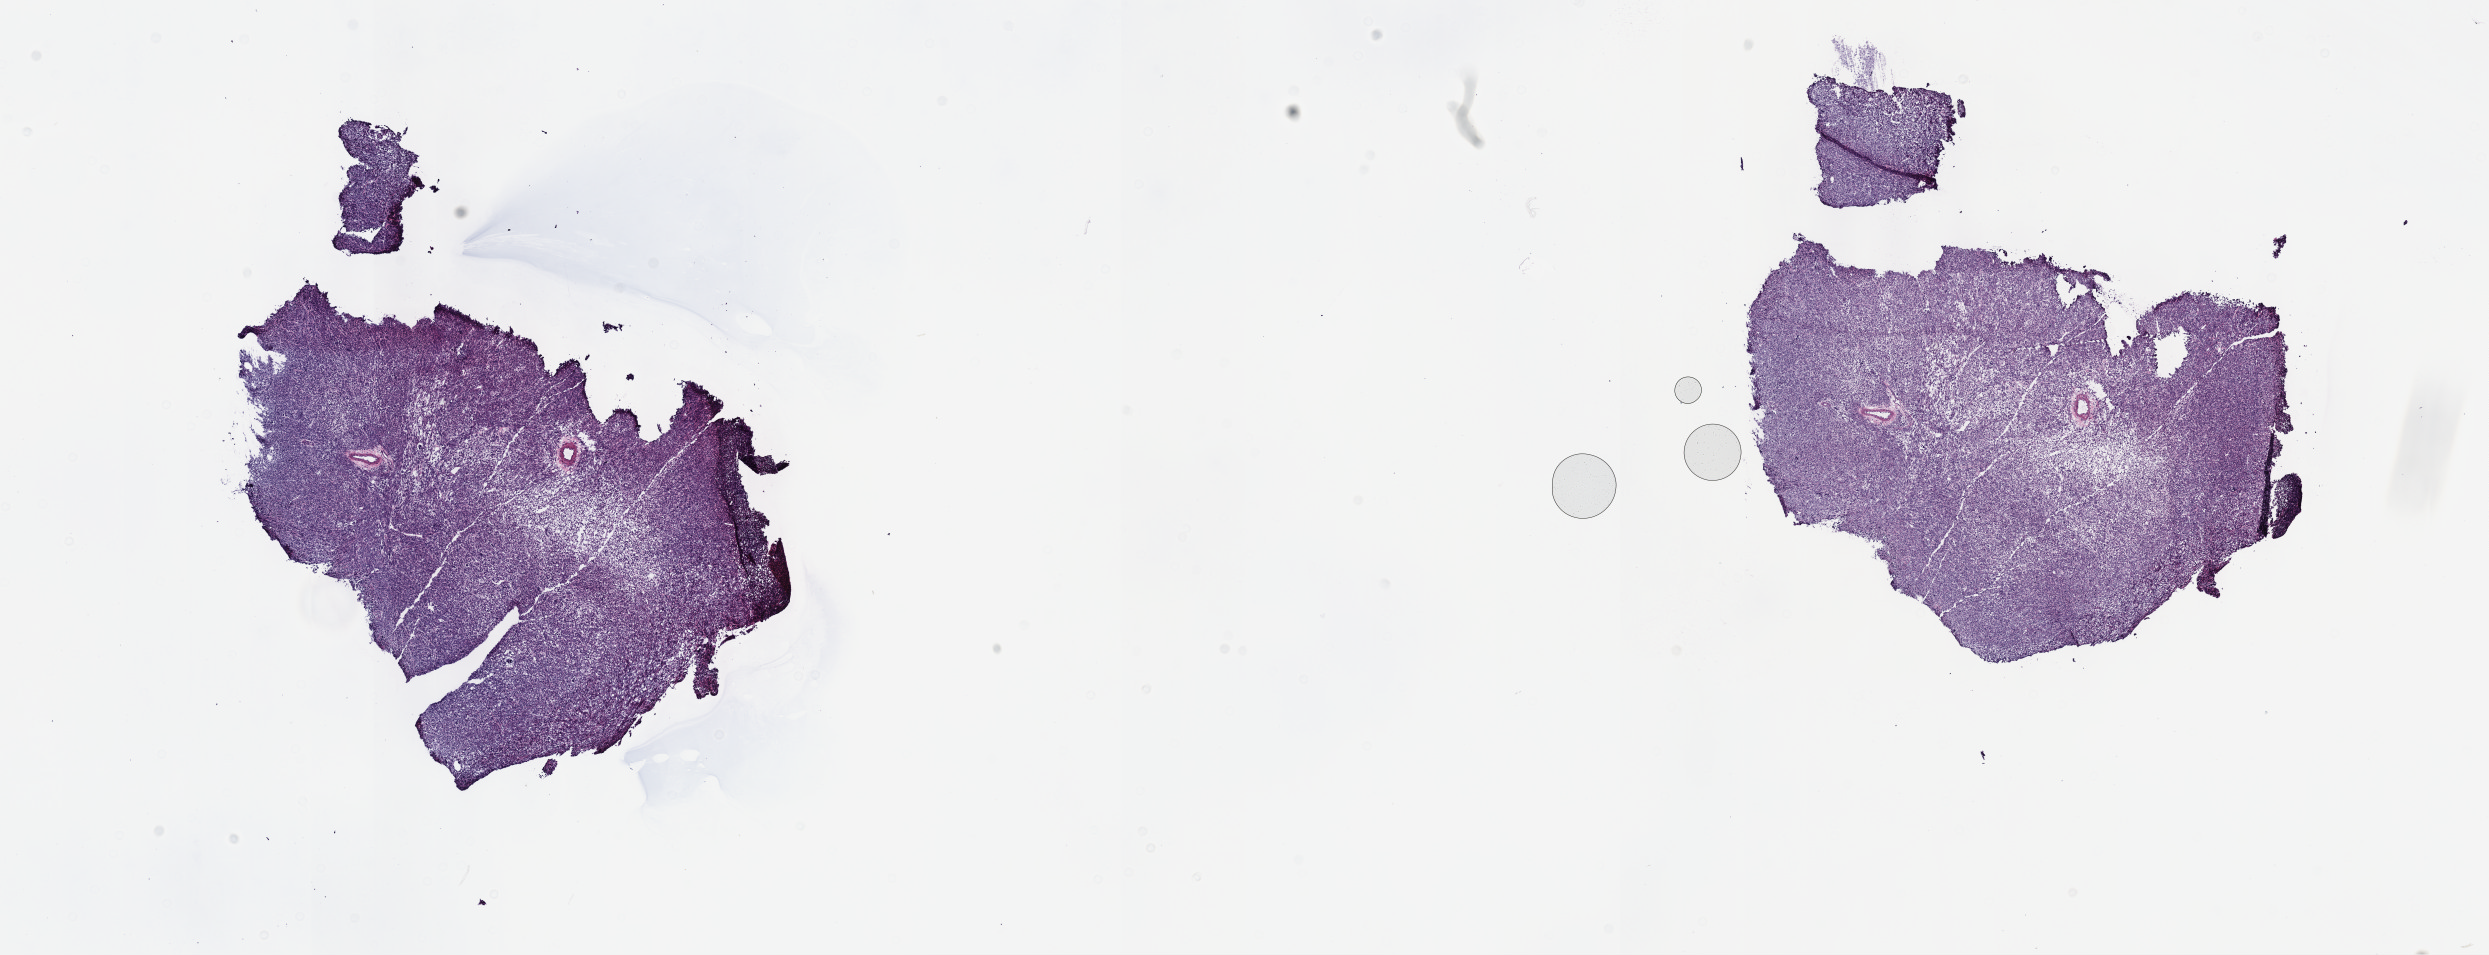
Digitized Hematoxylin and eosin (H&E) stained tissue section (whole slide), low-resolution overview of the scanned area, about 20.1 x 7.7 mm; frozen section from the top of the tissue portion; sample: primary tumour, uterus. Female patient; age at initial diagnosis 49 years. Slide review estimates, as recorded: tumour cells 100%, tumour nuclei 80%, normal cells 0%, stromal cells 0%, necrosis 0%. Infiltration values recorded for this section: lymphocyte infiltration 1%, monocyte infiltration 0%, neutrophil infiltration 0%.
* histologic diagnosis: Leiomyosarcoma, NOS